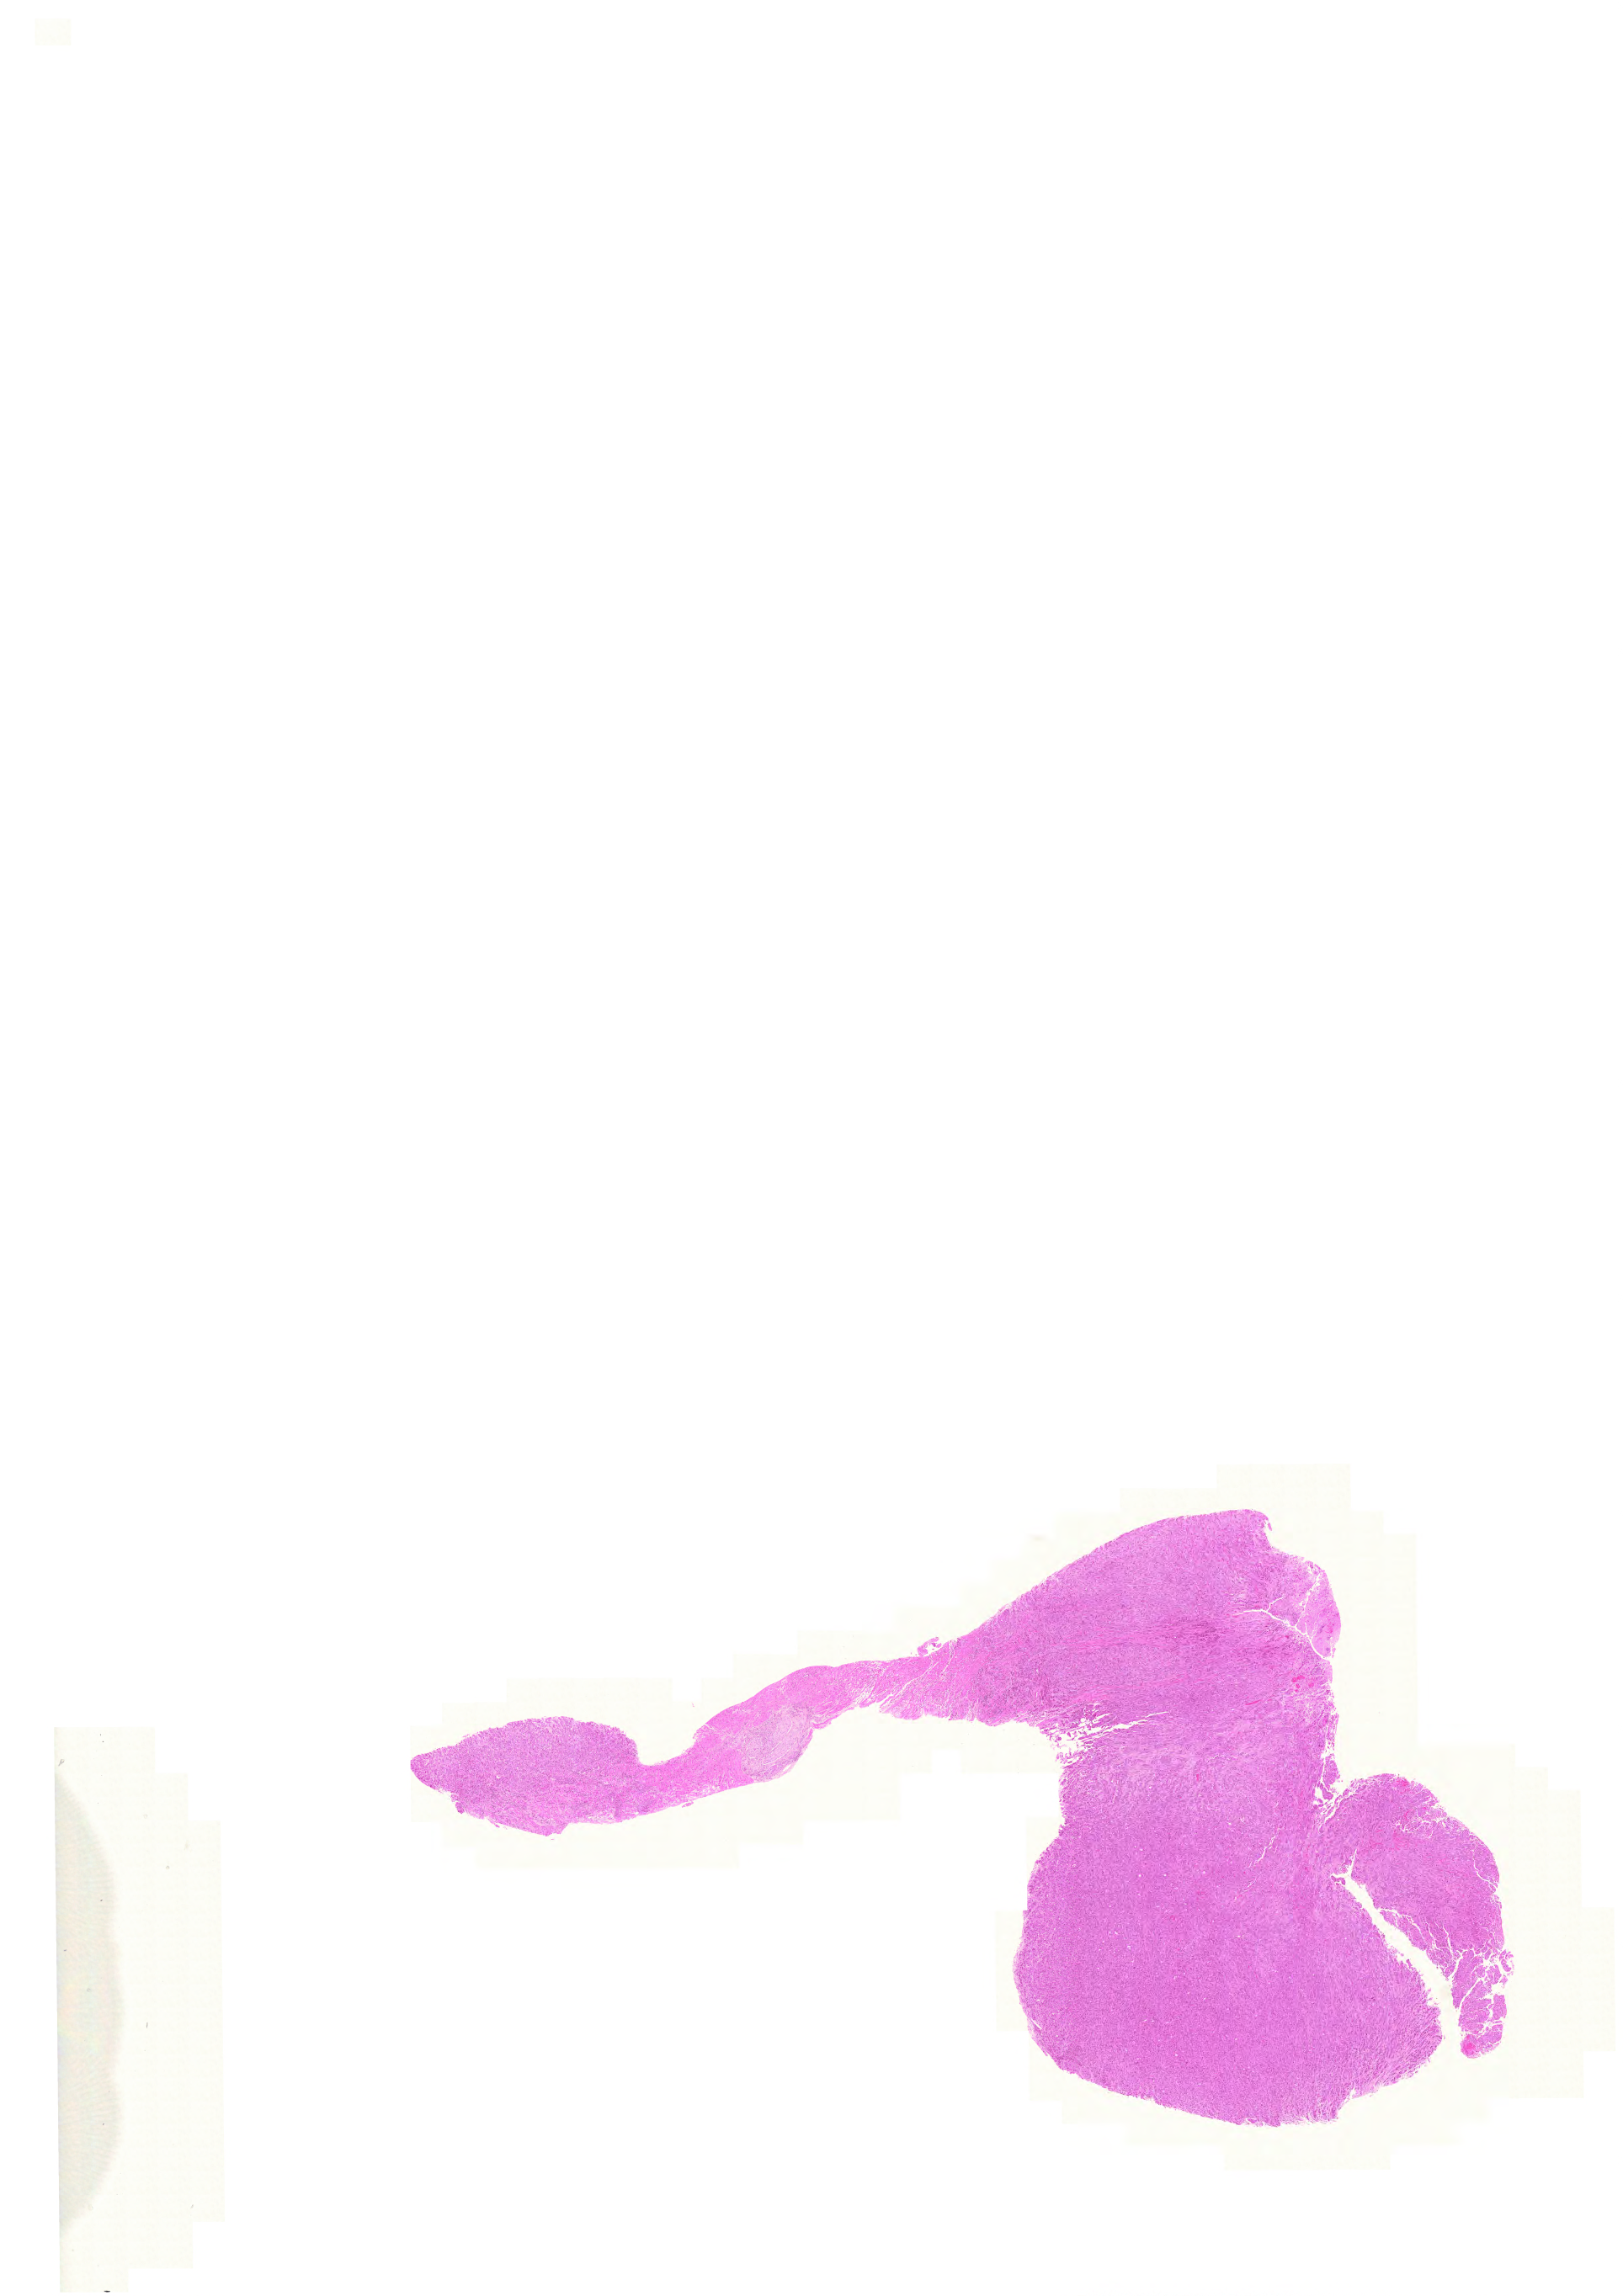
Digitized H&E-stained tissue section (whole slide), whole scanned area (about 14.3 x 20.3 mm, slide scanned at 20x) shown as a low-resolution overview. Formalin-fixed paraffin-embedded (FFPE) diagnostic section. Sample: primary tumour, rectum. Male, age 51 years at initial diagnosis.
TNM: T3 N0 M0. Lymph nodes positive (case pathology): 0 of 31 examined. AJCC pathologic stage: II (5th edition). Histologic diagnosis: Adenocarcinoma, NOS.